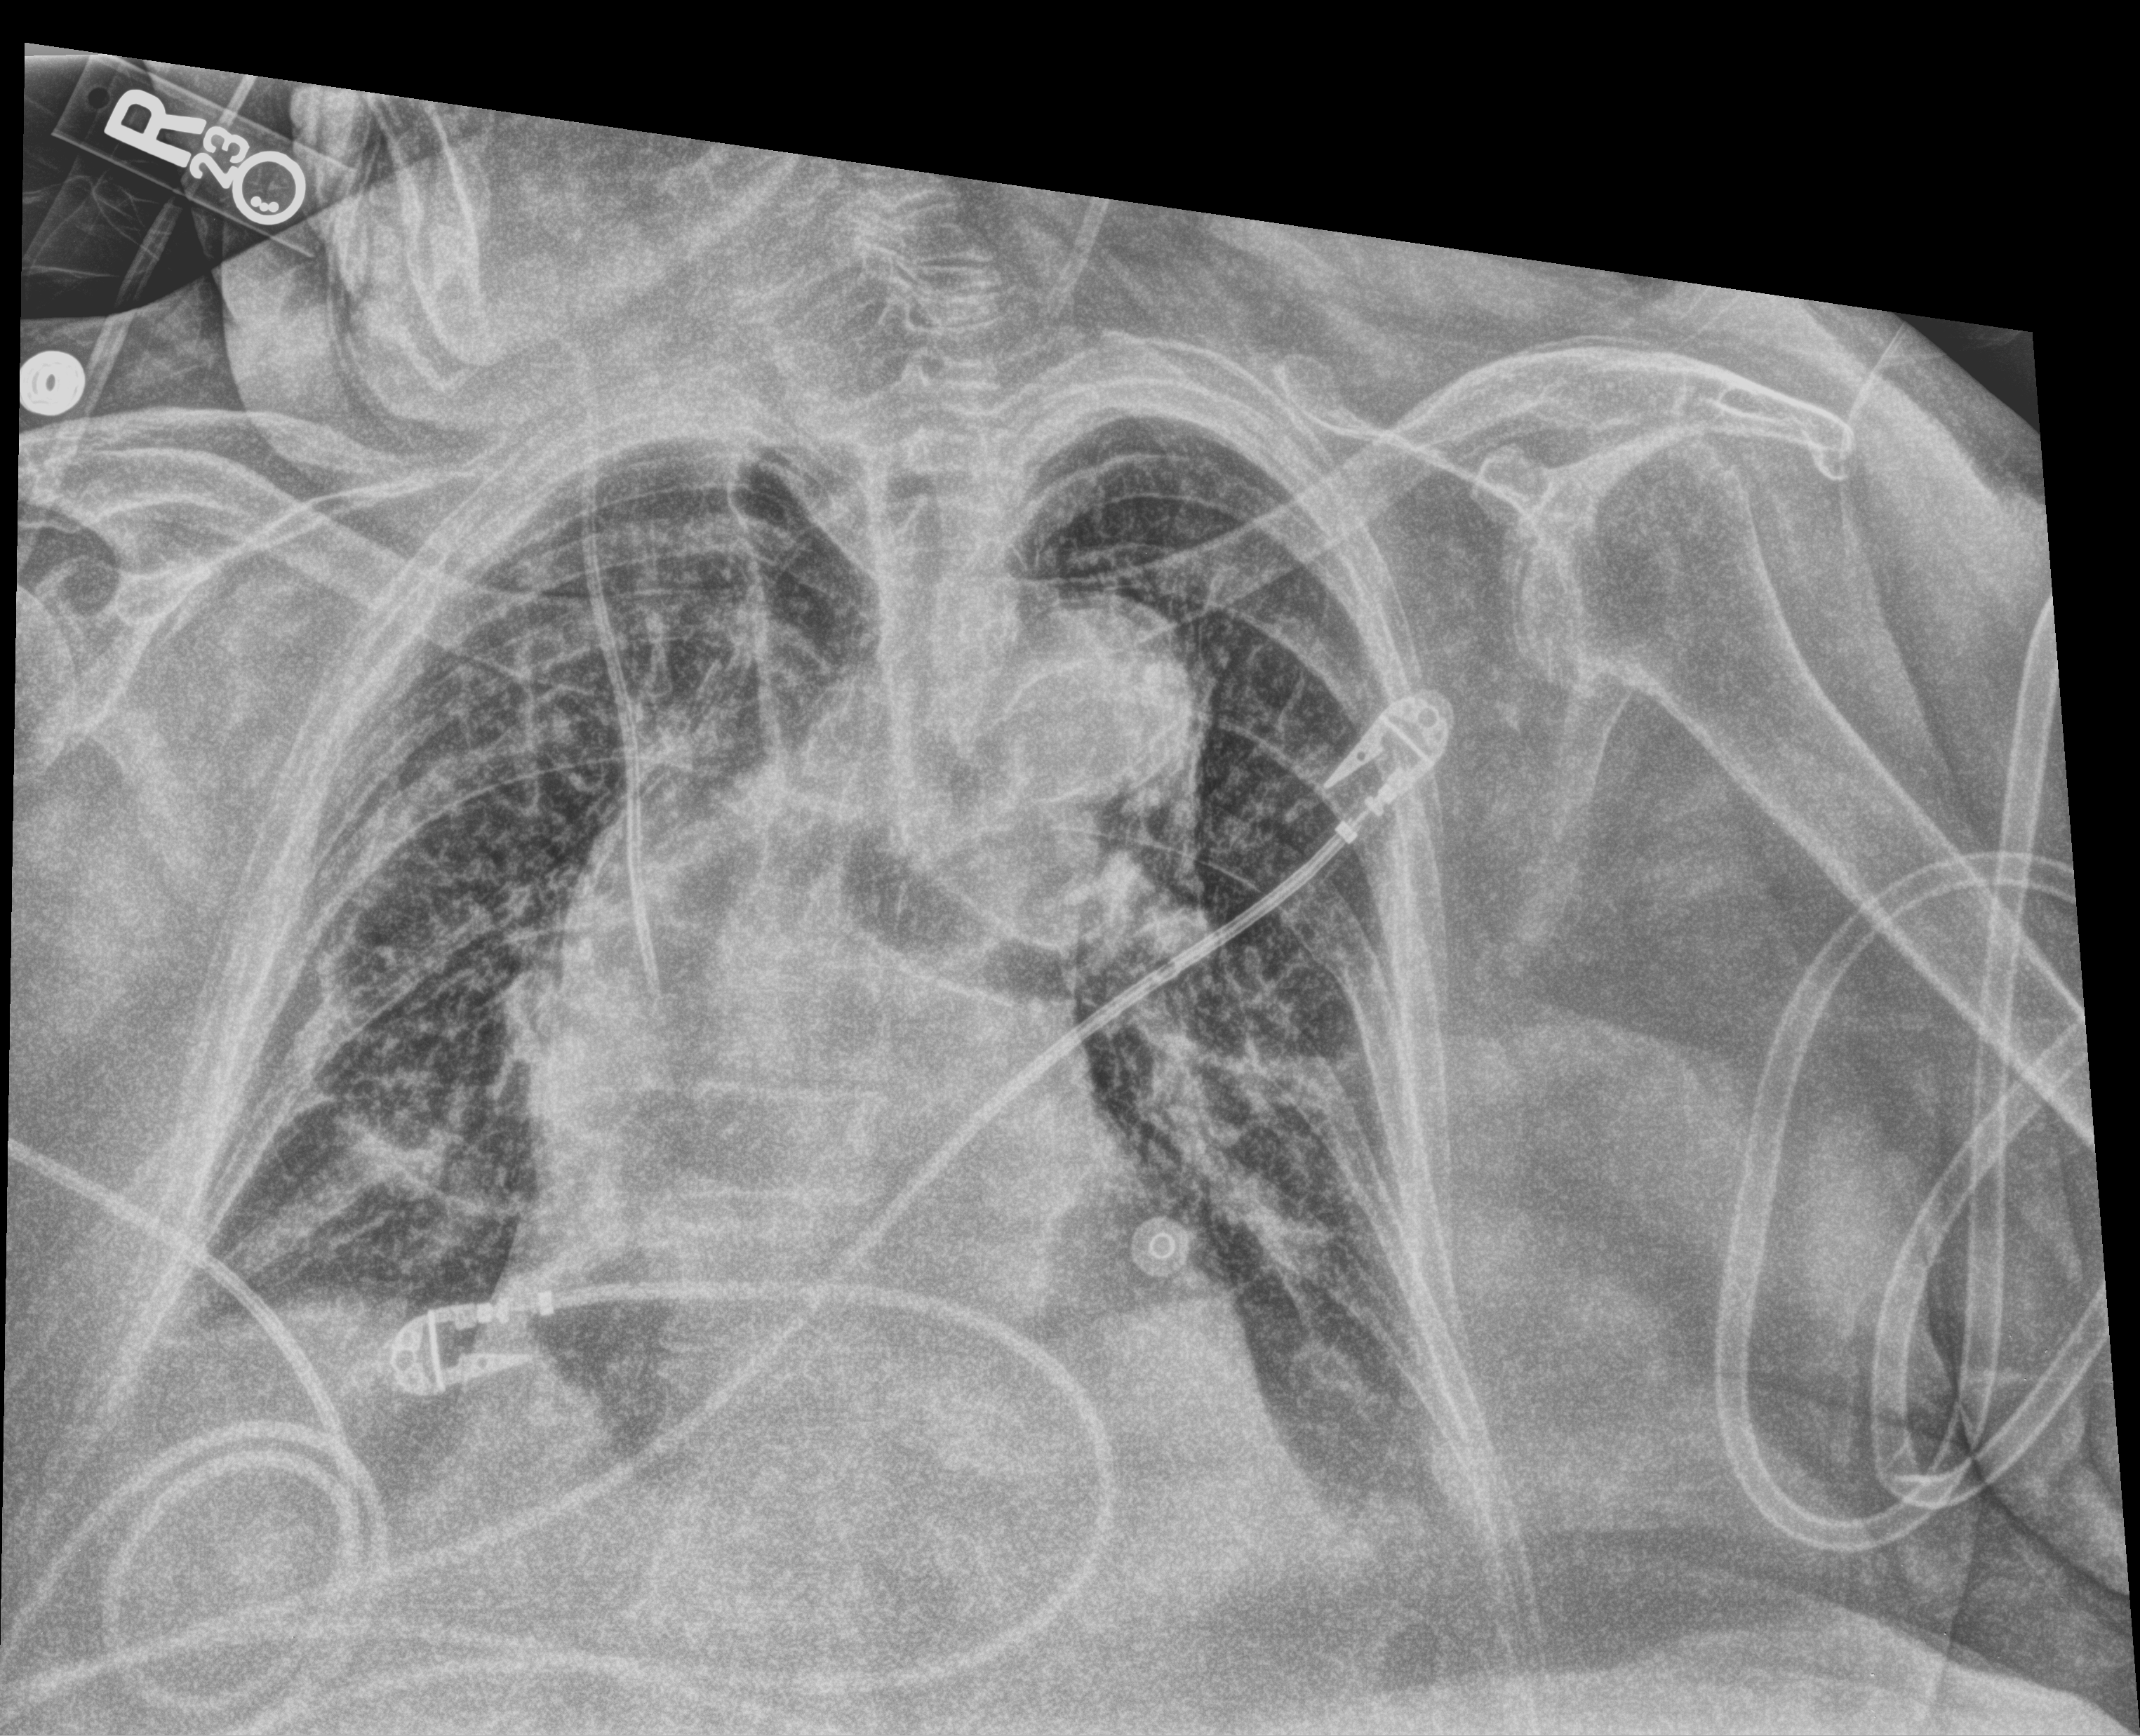
Chest X-ray (portable); anteroposterior (AP) projection. Female patient hospitalised with COVID-19, age 75–90 years.
Hospital-stay facts (about this admission, not read from this image; timing relative to this image not recorded): admitted to intensive care during this hospital stay: yes; length of hospital stay: 12 days.